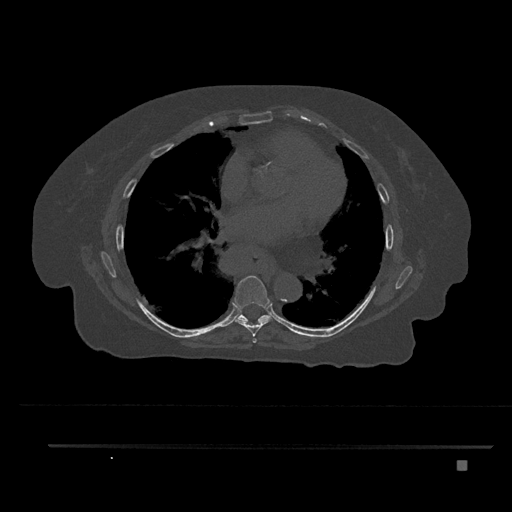
CT including the spine, one axial slice. Slice 471 of 797 in the series (ordered by position). Reconstruction kernel Br40s/3. 120 kVp. Bone window (W 1800 / L 400 HU). 0.5 mm slice thickness. 512 × 512 image matrix. Female patient, age 76 years. Case-level facts recorded for this patient, not image findings: primary cancer: lung.
Outlined on this slice (semi-automatic segmentation, software-assisted and operator-edited):
- T6 vertebra: box from (x=252, y=339) to (x=257, y=343) px
- T7 vertebra: (x=233, y=276)–(x=274, y=337)
- T8 vertebra: (x=236, y=313)–(x=270, y=321)